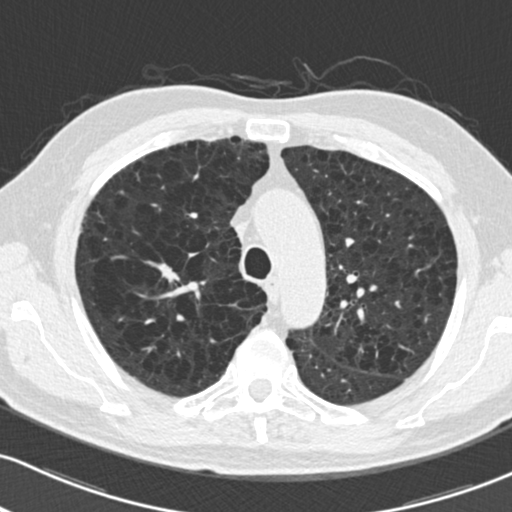
Chest CT (low-dose screening protocol), one axial image, second screening round (one year after baseline), lung window (W 1500 / L -600 HU), standard (soft-tissue) reconstruction kernel (B30f). Male participant, aged 73 years at enrolment. Current smoker at enrolment.
- Lesion marked by an expert reader, box from (x=149, y=257) to (x=195, y=290) px.
- Reader record for this screening exam (exam-level; its link to the box is not recorded): non-calcified nodule or mass ≥4 mm, right upper lobe, 10 × 9 mm, smooth margins, soft tissue attenuation, pre-existing on the prior screen: yes; interval growth: yes.
- Official screen result: positive, other.
- Lung cancer was diagnosed 51 days after this screen: squamous cell carcinoma, NOS, right upper lobe, stage IA (AJCC 6th edition), 10 mm at pathology.